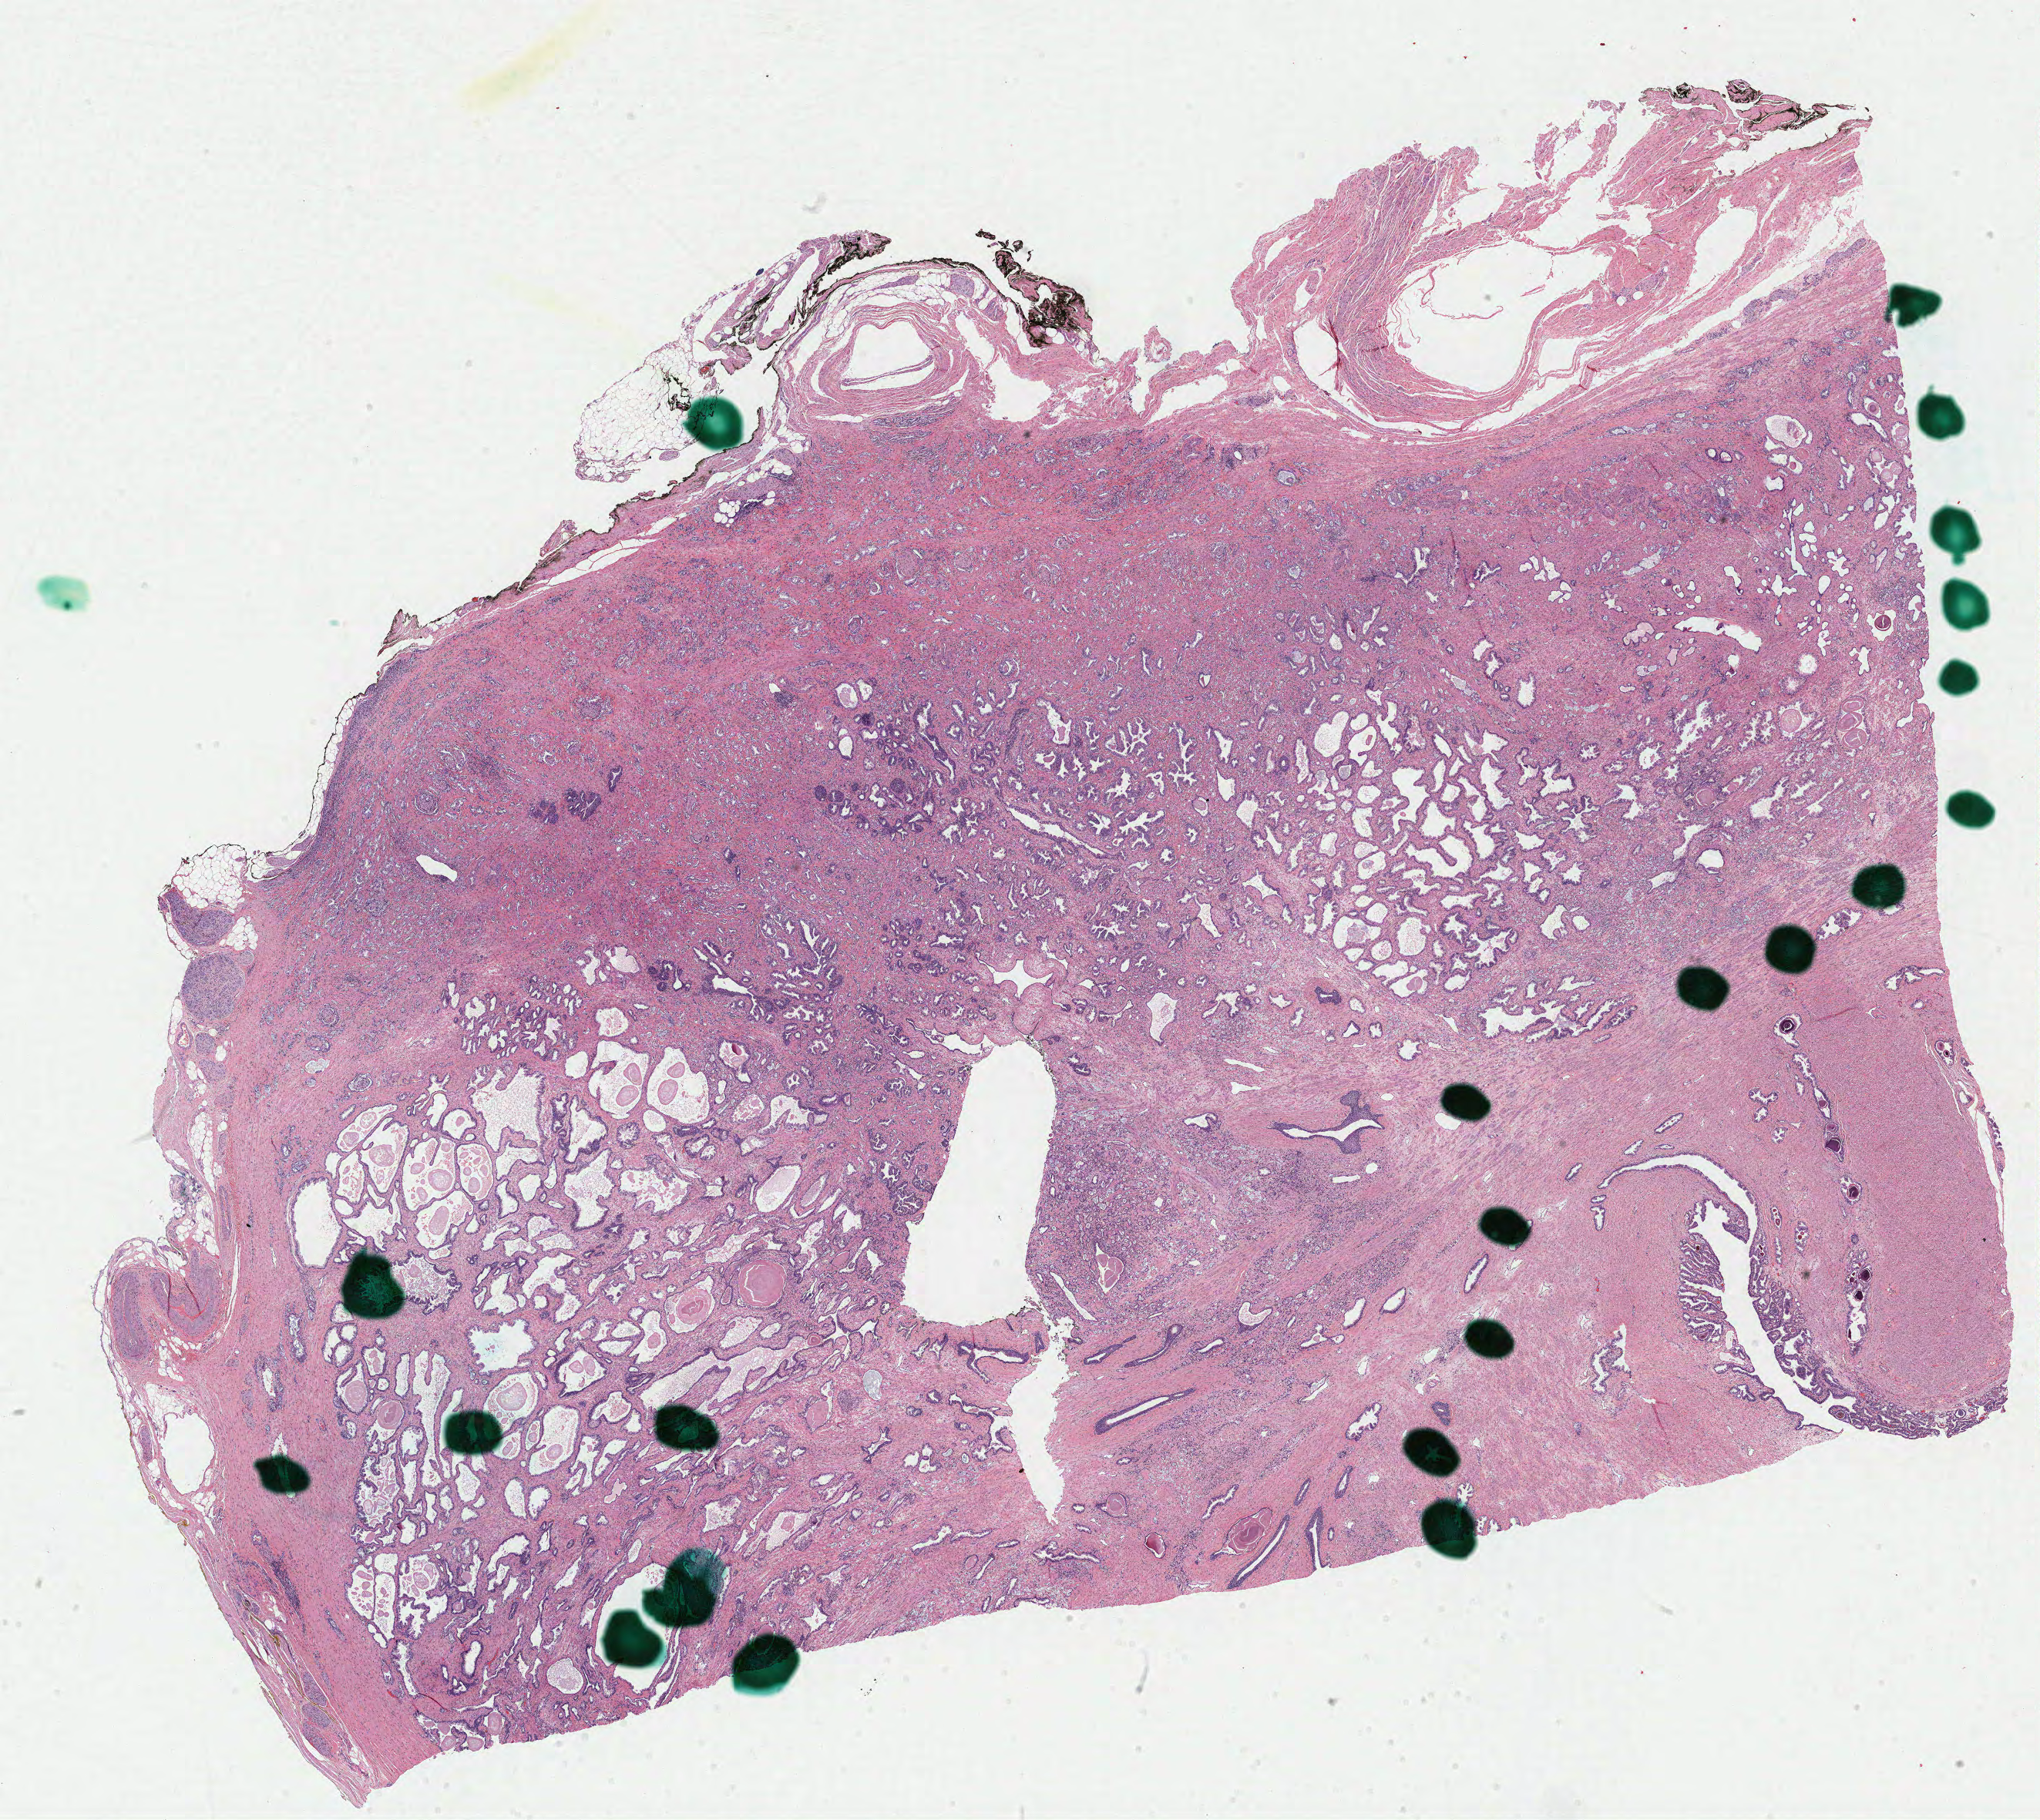
Digitized Hematoxylin and eosin (H&E) stained tissue section (whole slide), low-resolution overview of the scanned area, about 21.0 x 18.7 mm (from a 40x scan). FFPE section. Sample: primary tumour, prostate. Male patient; age at initial diagnosis 65 years. Gleason score: 9 (4+5).
Pathologic diagnosis: Adenocarcinoma, NOS (prostate gland). Laterality: bilateral.